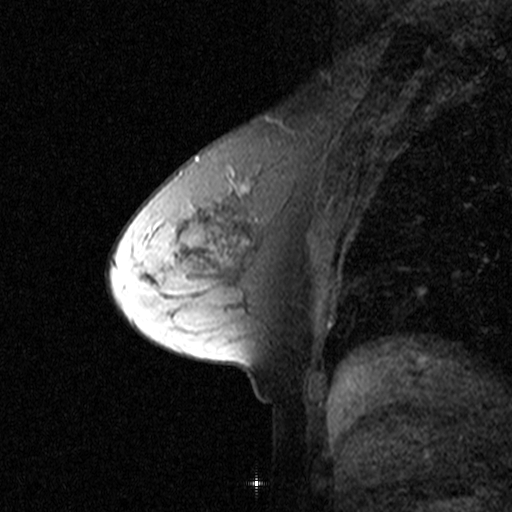
Breast MRI (dynamic contrast-enhanced), one sagittal slice; position 20 of 44 along the scan axis; dynamic contrast-enhanced study with each time point stored as its own series, time point 2 of 3 at this slice position (early post-contrast, ordered by acquisition time); 1.5 T; TE 4.5 ms, TR 11 ms; 512 × 512 image matrix, field of view 200 × 200 mm. Patient: female, 53 years. Case-level facts recorded for this patient, not image findings: setting: breast cancer imaged before/during neoadjuvant chemotherapy; receptor status: HR-positive, HER2-negative.
Outlined on this slice (semi-automatic segmentation, software-assisted and operator-edited):
- analysis volume of interest (the breast-tissue region the enhancement analysis was run in; not a lesion): bounding box <170,150,277,273> (left, top, right, bottom; pixels)
- tumour enhancement mask (voxels above the 90 % enhancement threshold inside the analysis volume of interest): <195,155,251,249>